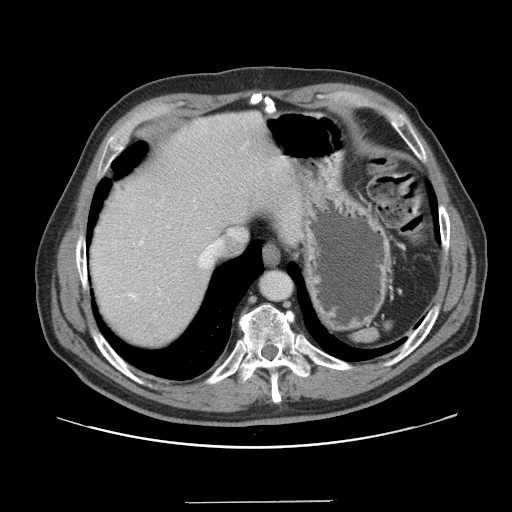
Contrast-enhanced abdominal CT, one axial slice; slice 132 of 151 in the series (ordered by position); soft-tissue window (W 400 / L 40 HU); 2.5 mm slice thickness; 512 × 512 image matrix, field of view 399 × 399 mm. Male patient, age 63 years. Case-level facts recorded for this patient, not image findings: diagnosis: colorectal cancer liver metastases, imaged before liver resection; multiple liver metastases: no; largest metastasis: 2.1 cm; disease in both lobes: no.
Structures marked on this image (outlined manually by an expert reader):
- hepatic veins: box from (x=200, y=241) to (x=221, y=266) px
- liver: (x=89, y=112)–(x=305, y=349)
- planned liver remnant (the part of the liver to remain after resection): (x=90, y=127)–(x=245, y=350)